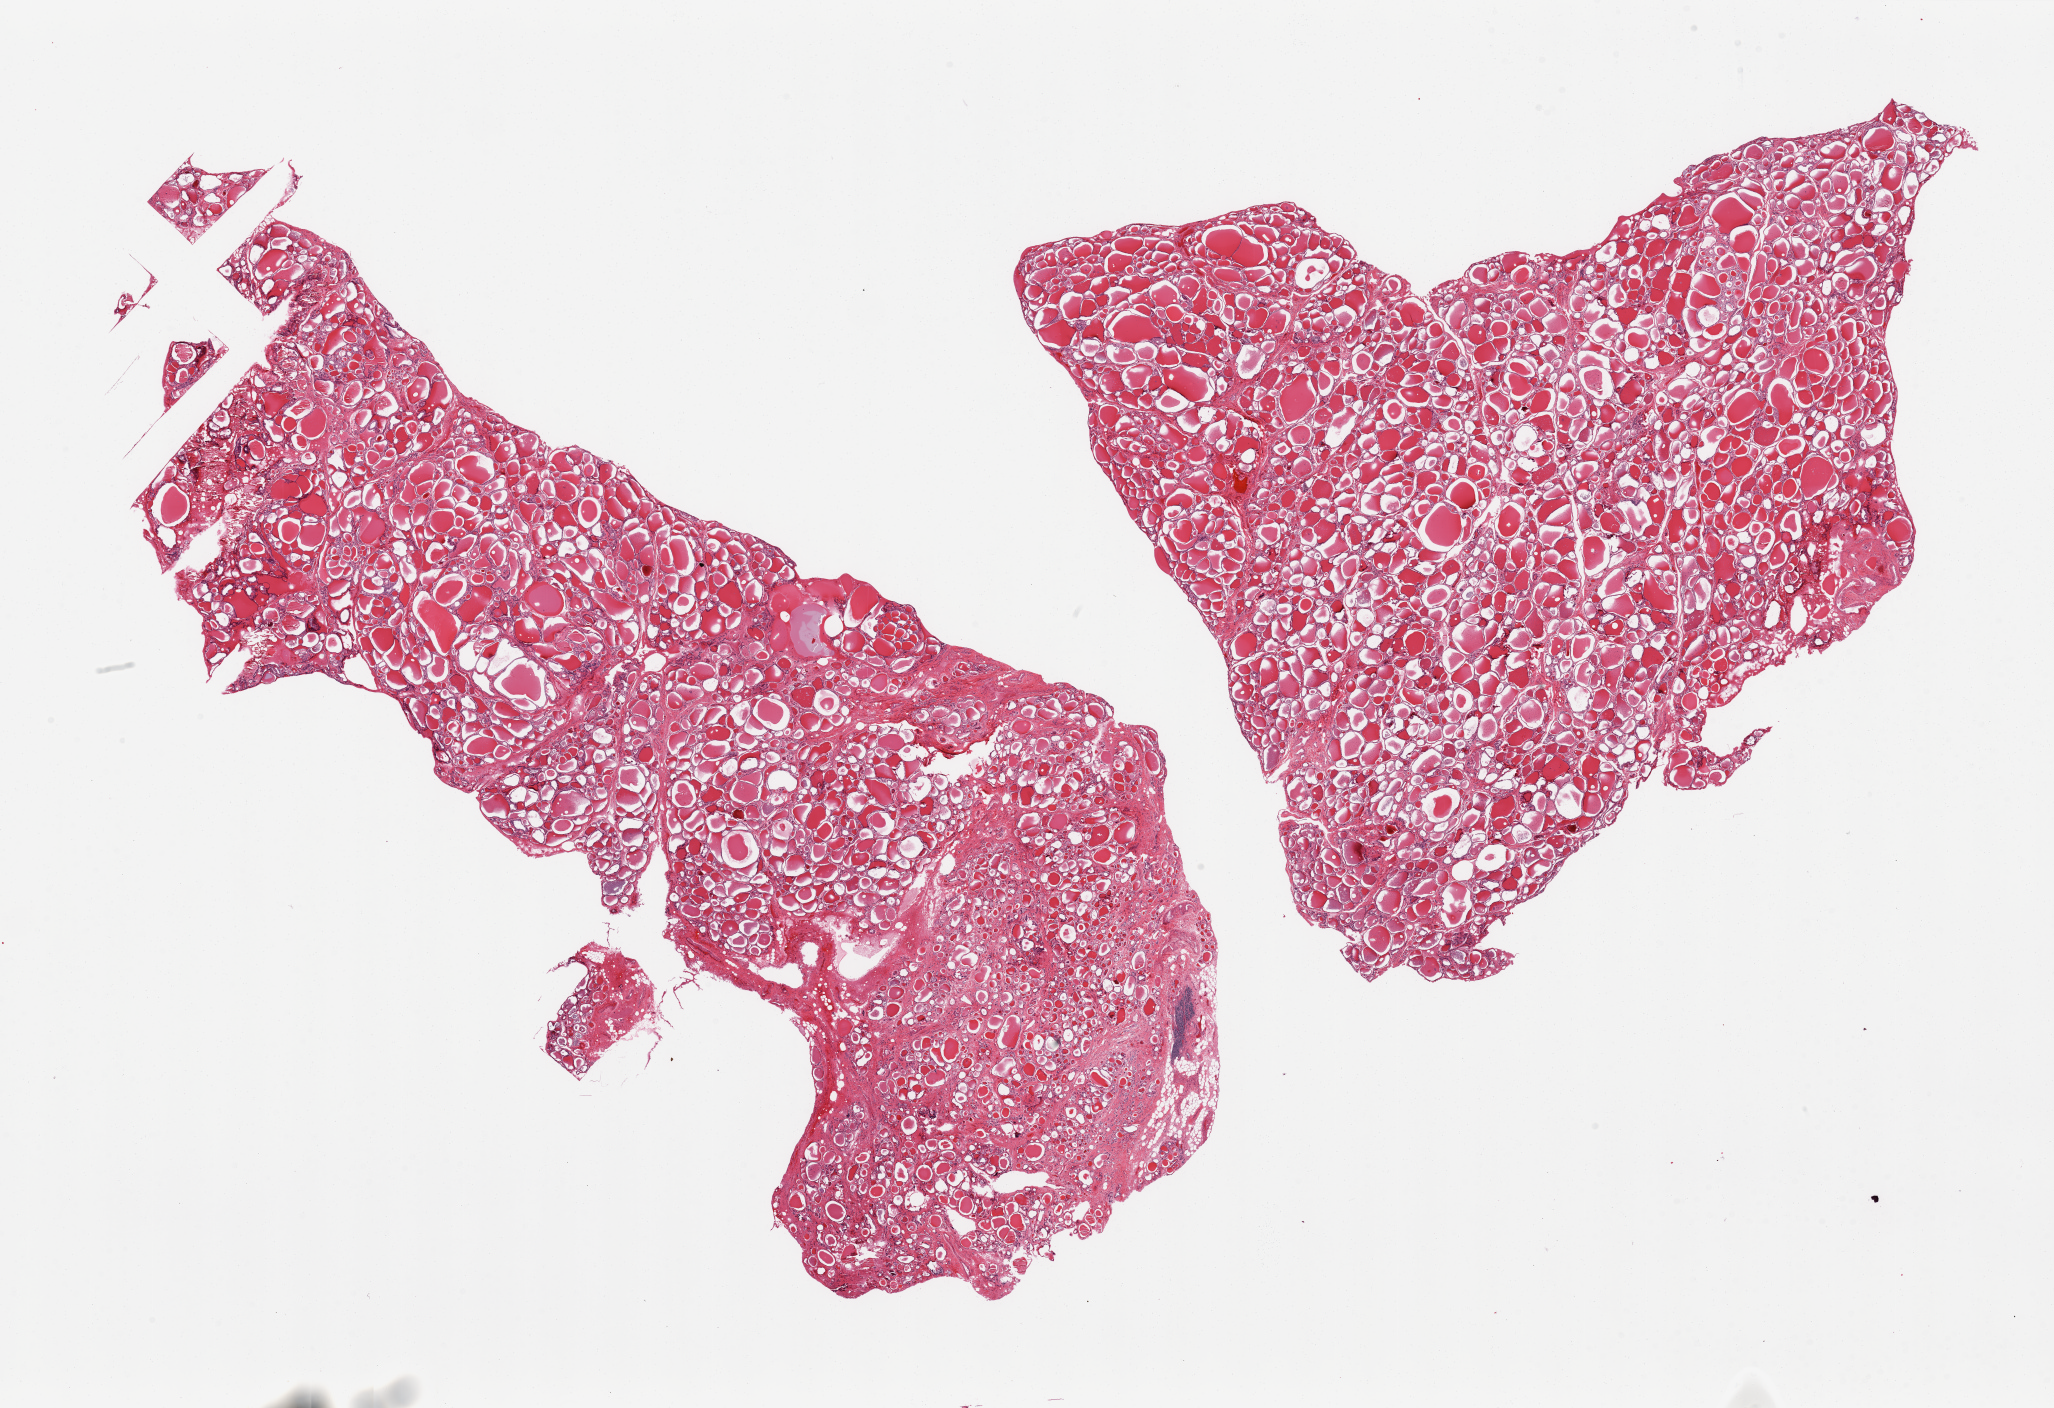
Digitized haematoxylin and eosin-stained section, whole scanned area (about 32.5 x 22.3 mm) shown as a low-resolution overview; PAXgene-fixed, paraffin-embedded tissue; section of thyroid (target tissue); tissue donor sample. Donor sex: male.
Reviewer comment on this tissue sample: 2 pieces, some nodularity/fibrosis, single collection of lymphocytes.